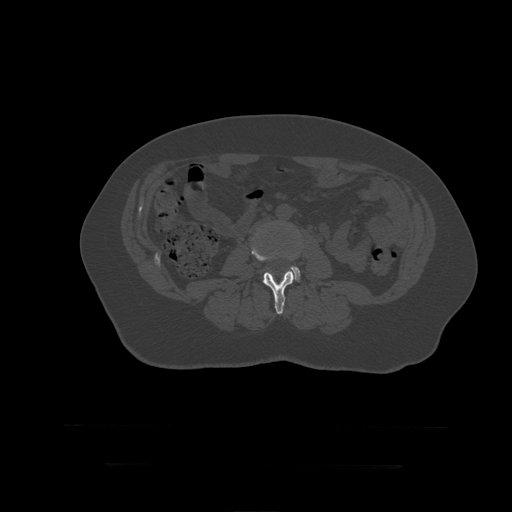
CT including the spine, one axial slice. Slice 114 of 399 in the series (ordered by position). Reconstruction kernel STANDARD. Bone window (W 1800 / L 400 HU). 1.25 mm slice thickness. 512 × 512 image matrix, field of view 450 × 450 mm. Patient age 41 years. Case-level facts recorded for this patient, not image findings: primary cancer: breast.
Outlined on this slice (semi-automatic segmentation, software-assisted and operator-edited):
- L3 vertebra: box from (x=252, y=248) to (x=296, y=315) px
- L4 vertebra: (x=290, y=256)–(x=301, y=282)